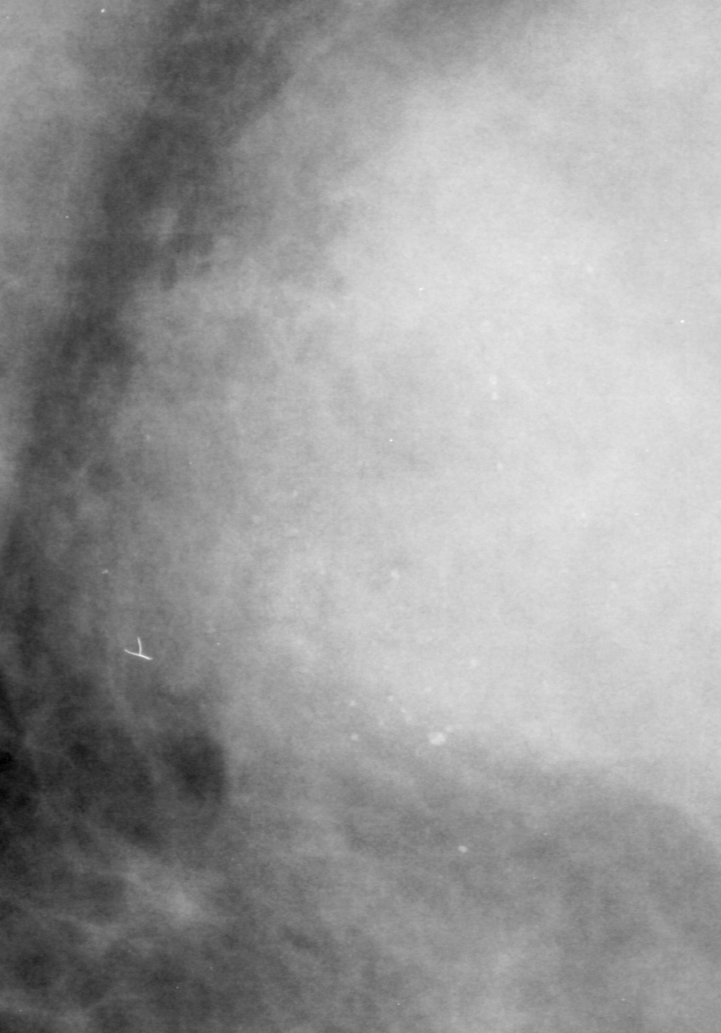
Region of interest cut from a scanned film mammogram (one marked finding), right breast, MLO view, BI-RADS breast density category 4 (scale 1–4).
Calcifications, morphology amorphous, distribution segmental; BI-RADS assessment category 4; subtlety rating 3 on a 1 (subtle) to 5 (obvious) scale; pathology result (as recorded, not read from the image): benign.